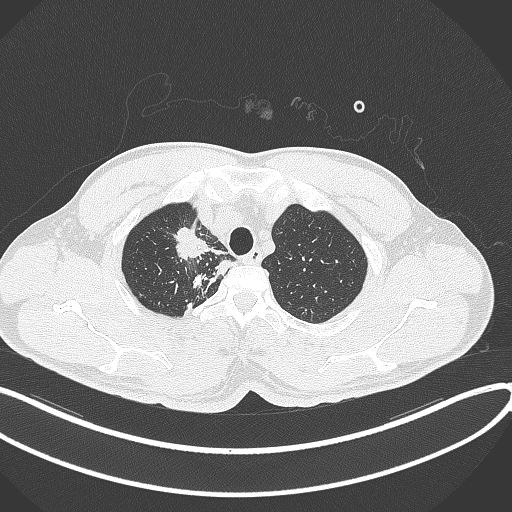
Chest CT, one axial slice; slice 325 of 391 in the series (ordered by position); 120 kVp; lung window (W 1500 / L -600 HU); 1 mm slice thickness; 512 × 512 image matrix. Patient: male, 48 years. From the clinical record (not read from this slice): clinical TNM (as recorded): T1c N1 M1.
Annotated regions visible in this slice (bounding box drawn by a radiologist):
- lung tumour (recorded histology: adenocarcinoma): box from (x=167, y=226) to (x=209, y=261) px